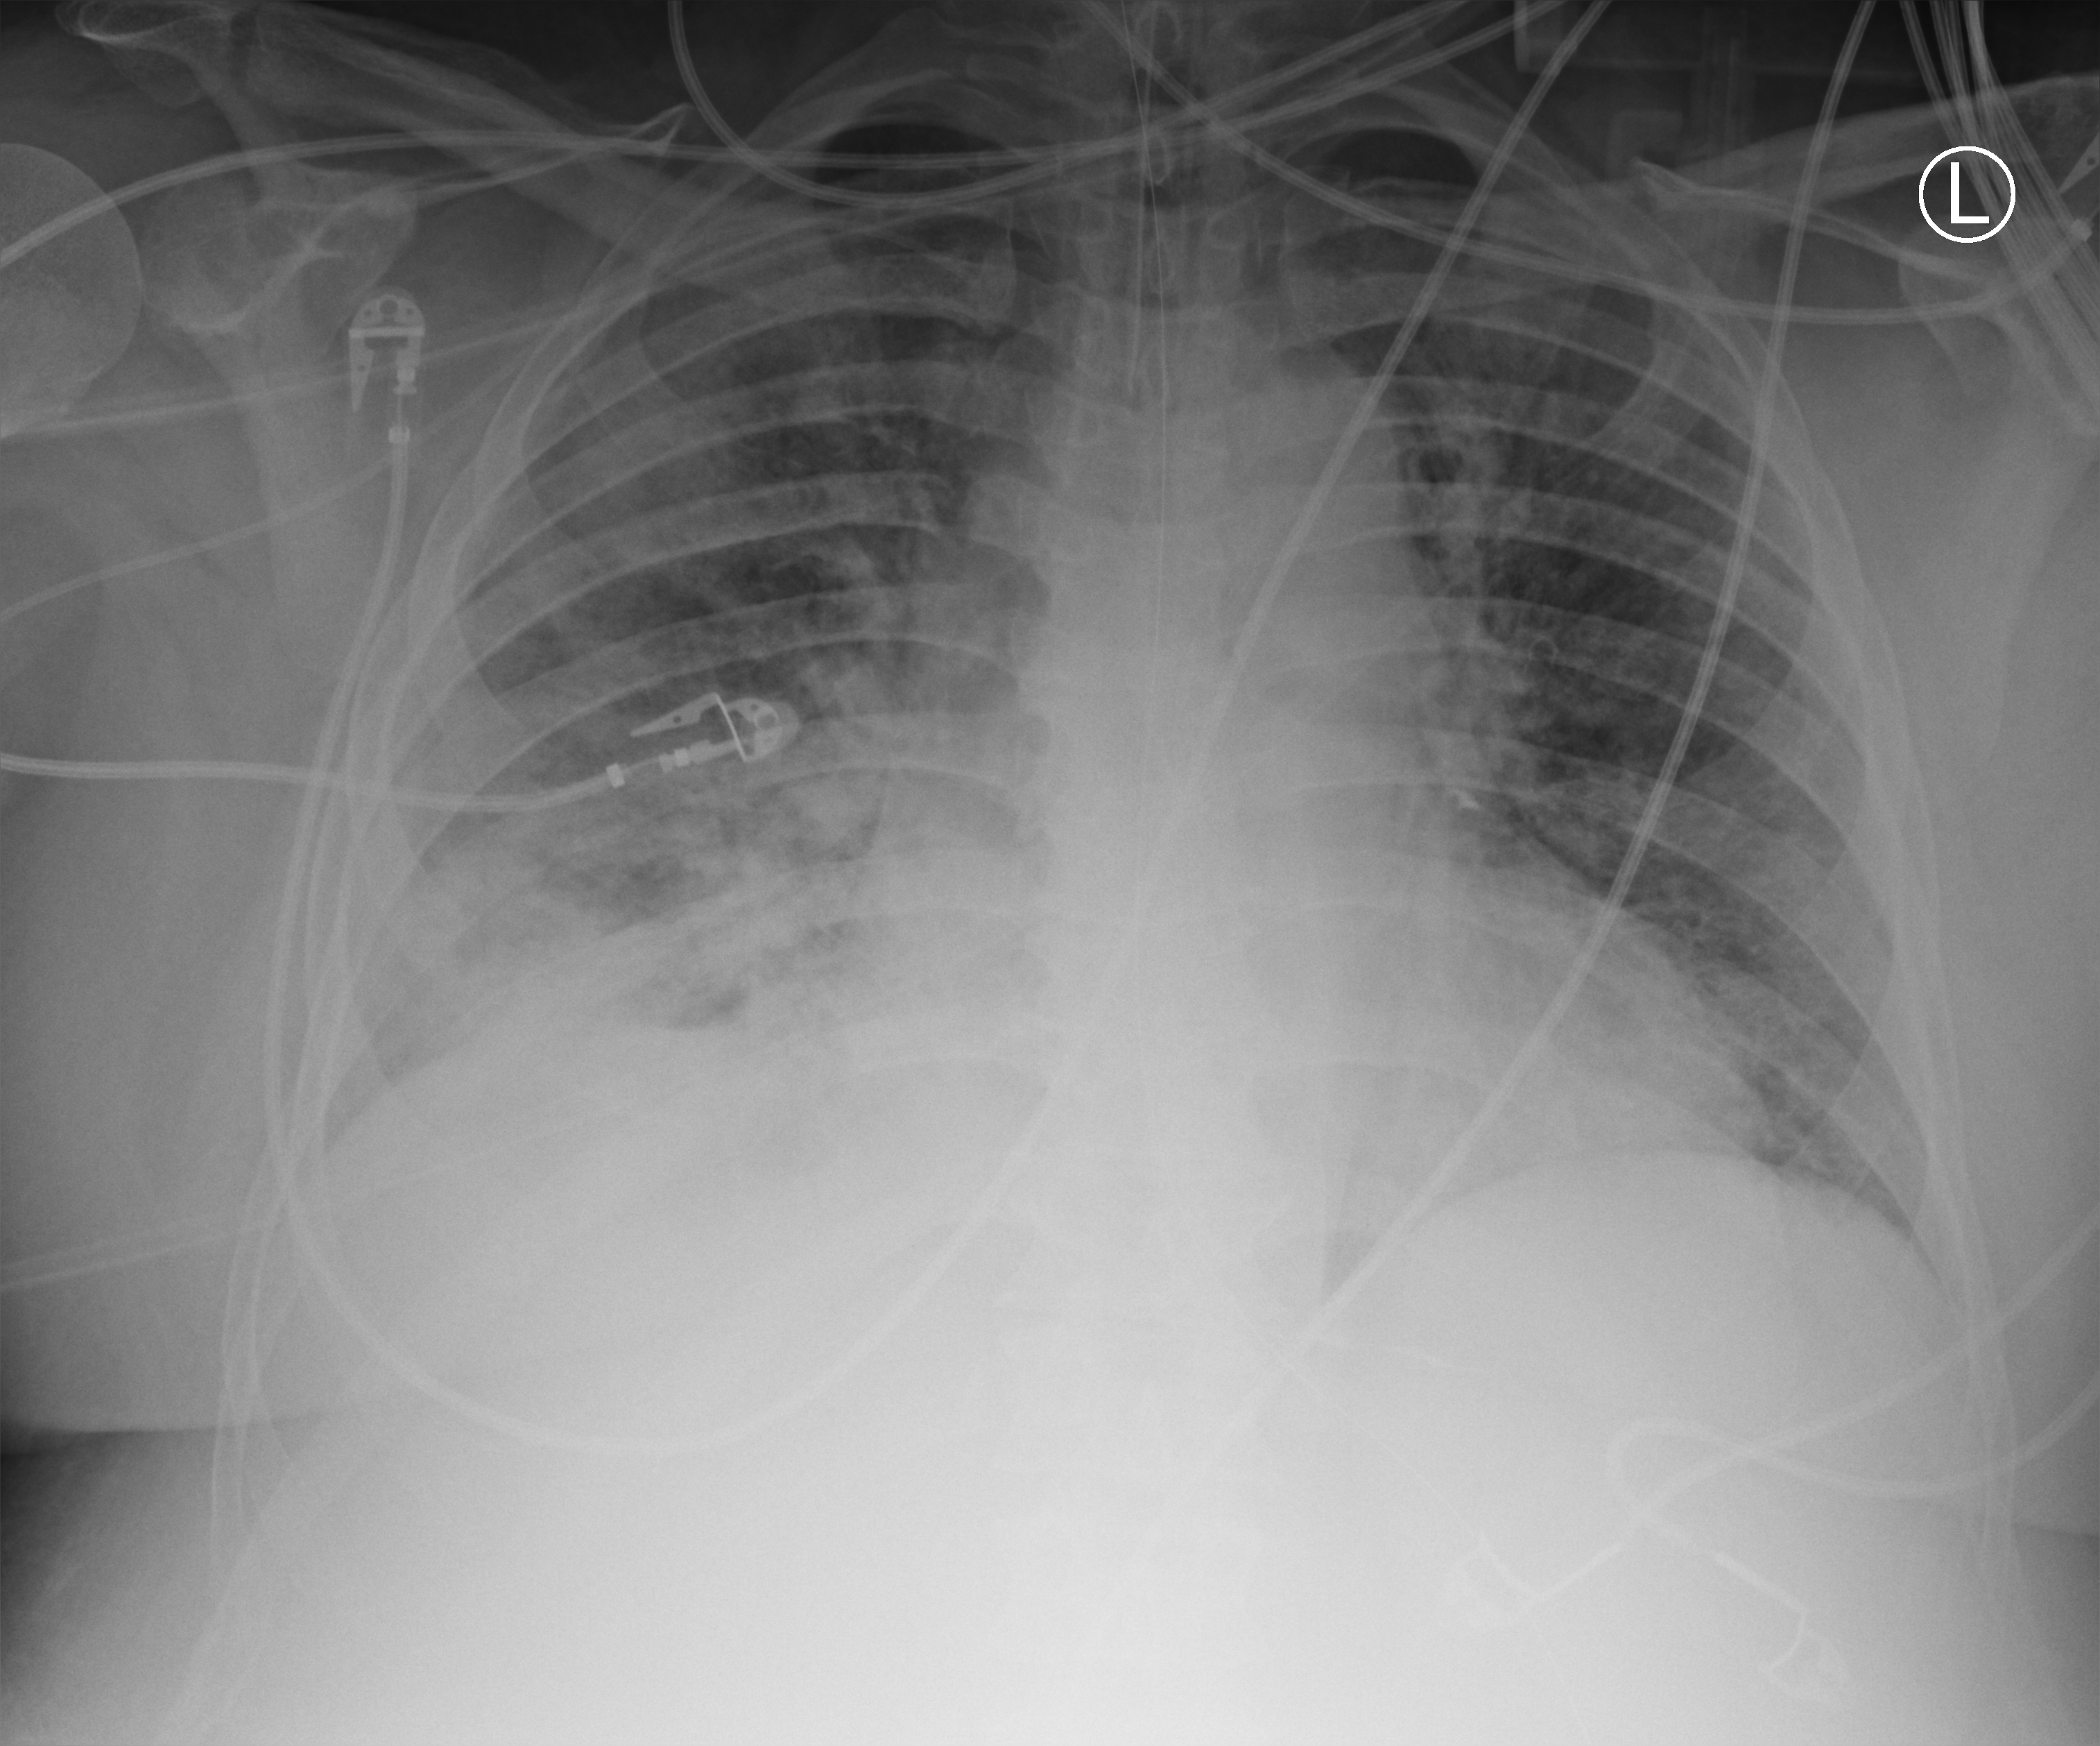
Chest X-ray (portable); anteroposterior (AP) projection. Patient hospitalised with COVID-19; male, aged 18–59 years.
From the hospital-stay record, not from the radiograph (when in the stay this image was taken is not recorded):
- length of hospital stay: 28 days
- mechanically ventilated during this hospital stay: yes